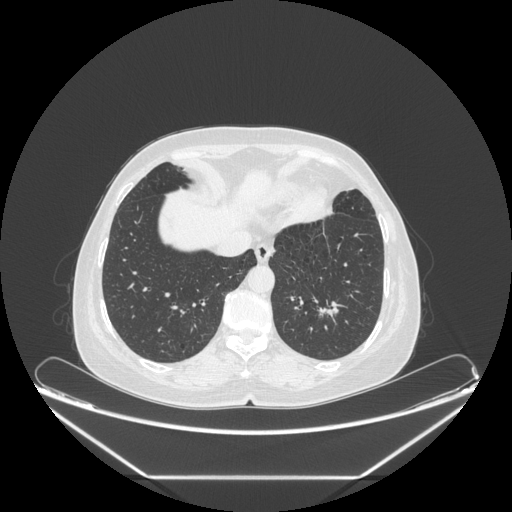
Chest CT, one axial slice; position 65 of 241 along the scan axis; reconstruction kernel STANDARD; 120 kVp; lung window (W 1500 / L -600 HU); 1.25 mm slice thickness; 512 × 512 image matrix, field of view 451 × 451 mm. Patient: female, 63 years. Case-level facts recorded for this patient, not image findings: clinical TNM (as recorded): T1c N0 M0; histopathological grade: G2-3.
Structures marked on this image (bounding box drawn by a radiologist):
- lung tumour (recorded histology: adenocarcinoma): bounding box (x1, y1, x2, y2) in pixels: (315, 295, 345, 330)